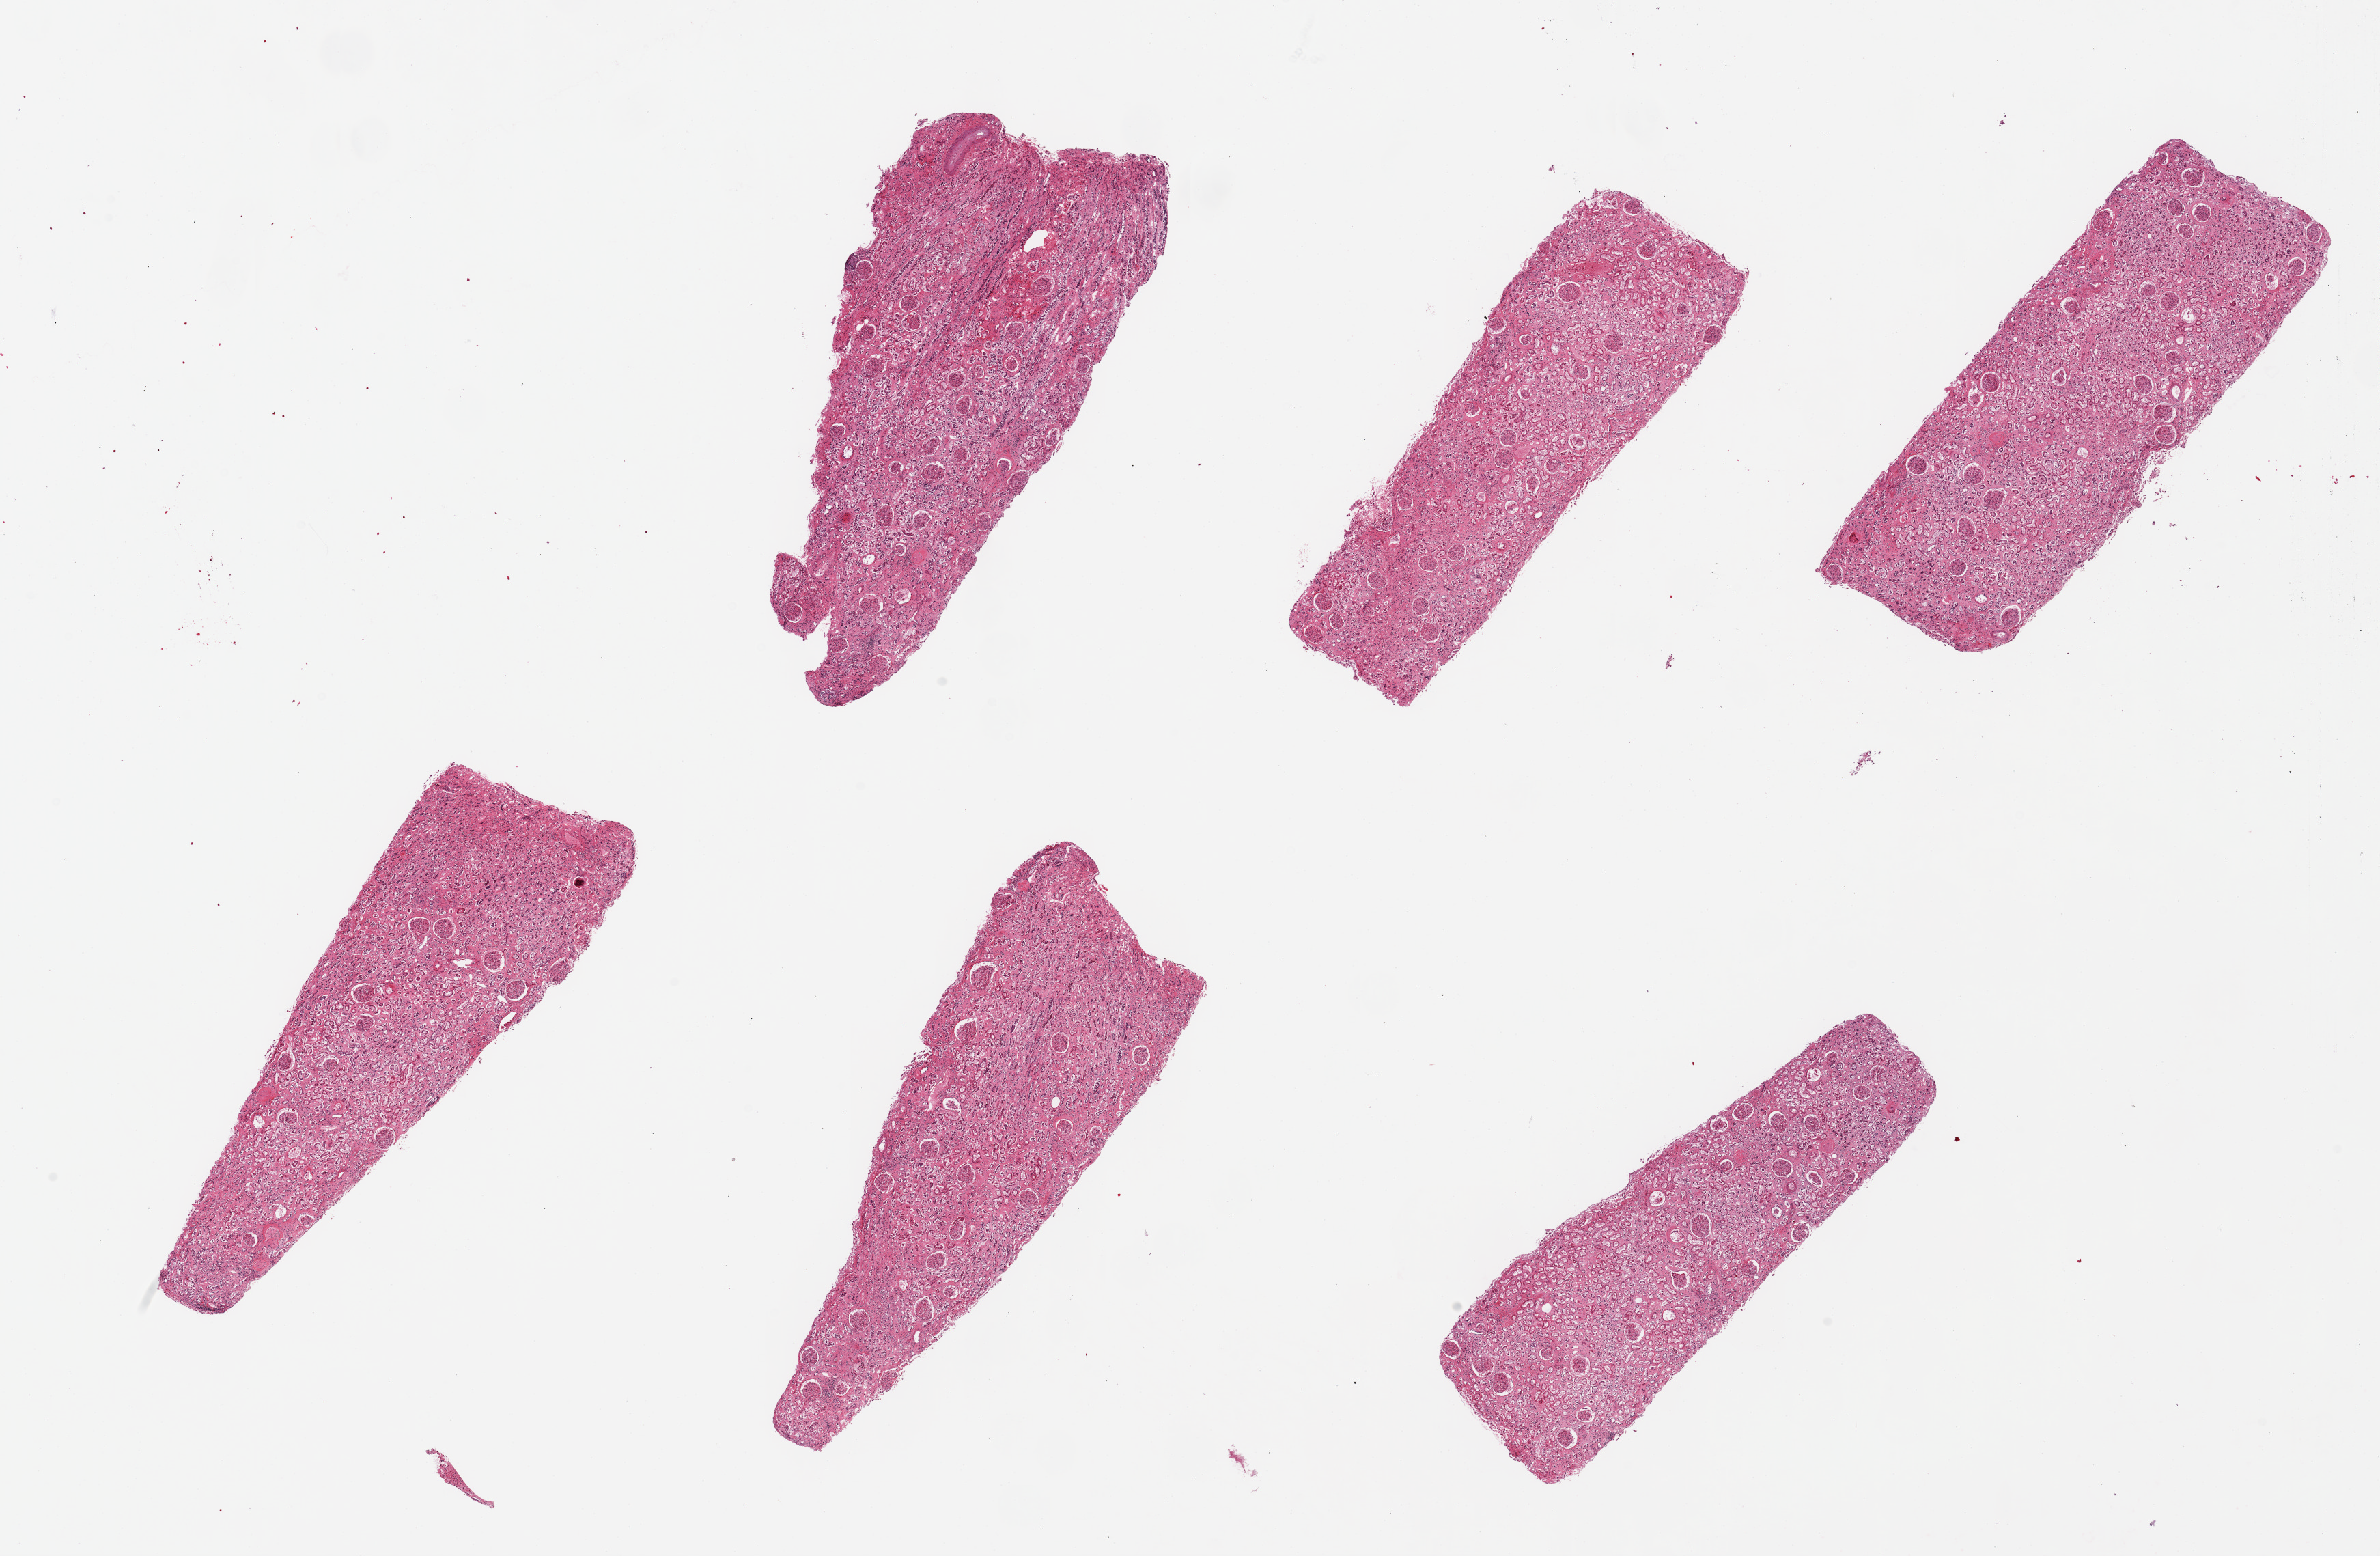
Digitized H&E-stained section — whole scanned area (about 27.6 x 18.0 mm, from a 20x scan) shown as a low-resolution overview. PAXgene-fixed paraffin-embedded (PFPE) section. Section of renal cortex (target tissue). Tissue donor sample. Male donor.
Pathologist's review note for this sample: 6 pieces, up to 7x3mm; Patchy glomerulosclerosis.